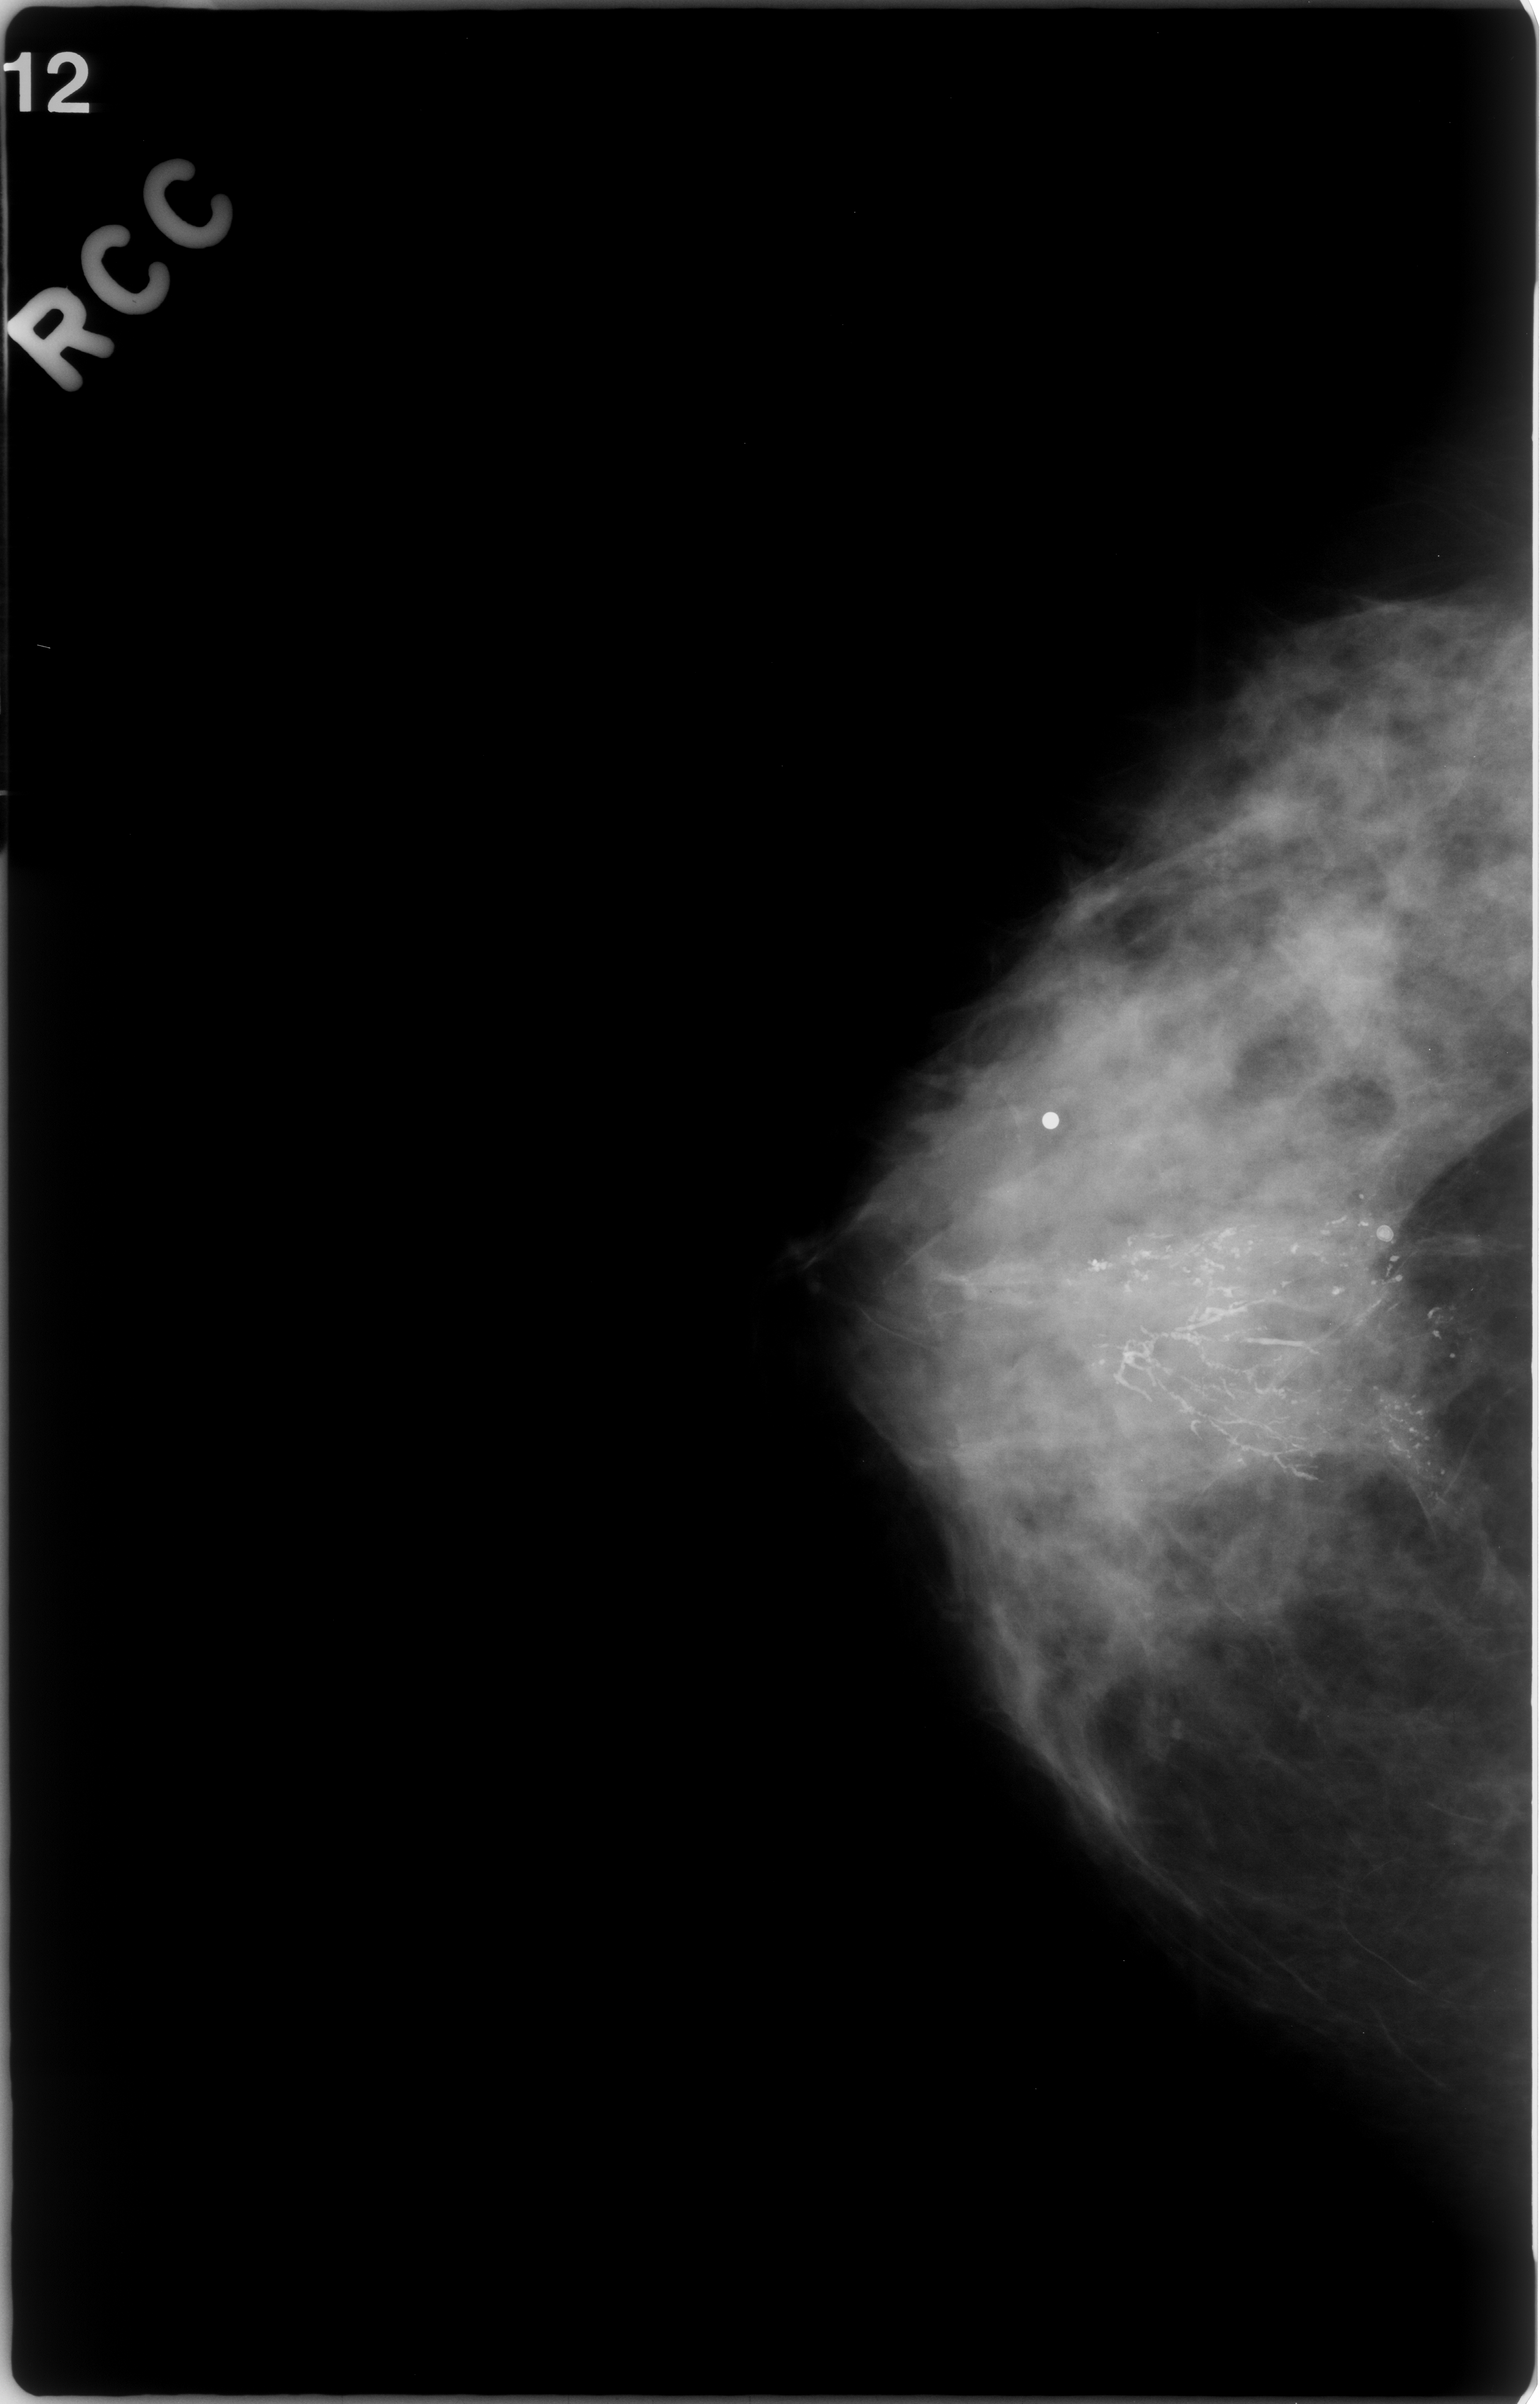
Mammogram (digitized film), right breast, CC view, BI-RADS breast density category 3 (scale 1–4).
- Marked abnormality: calcifications, morphology fine linear branching, distribution segmental; BI-RADS assessment category 5; subtlety rating 5 on a 1 (subtle) to 5 (obvious) scale; pathology result (as recorded, not read from the image): malignant.